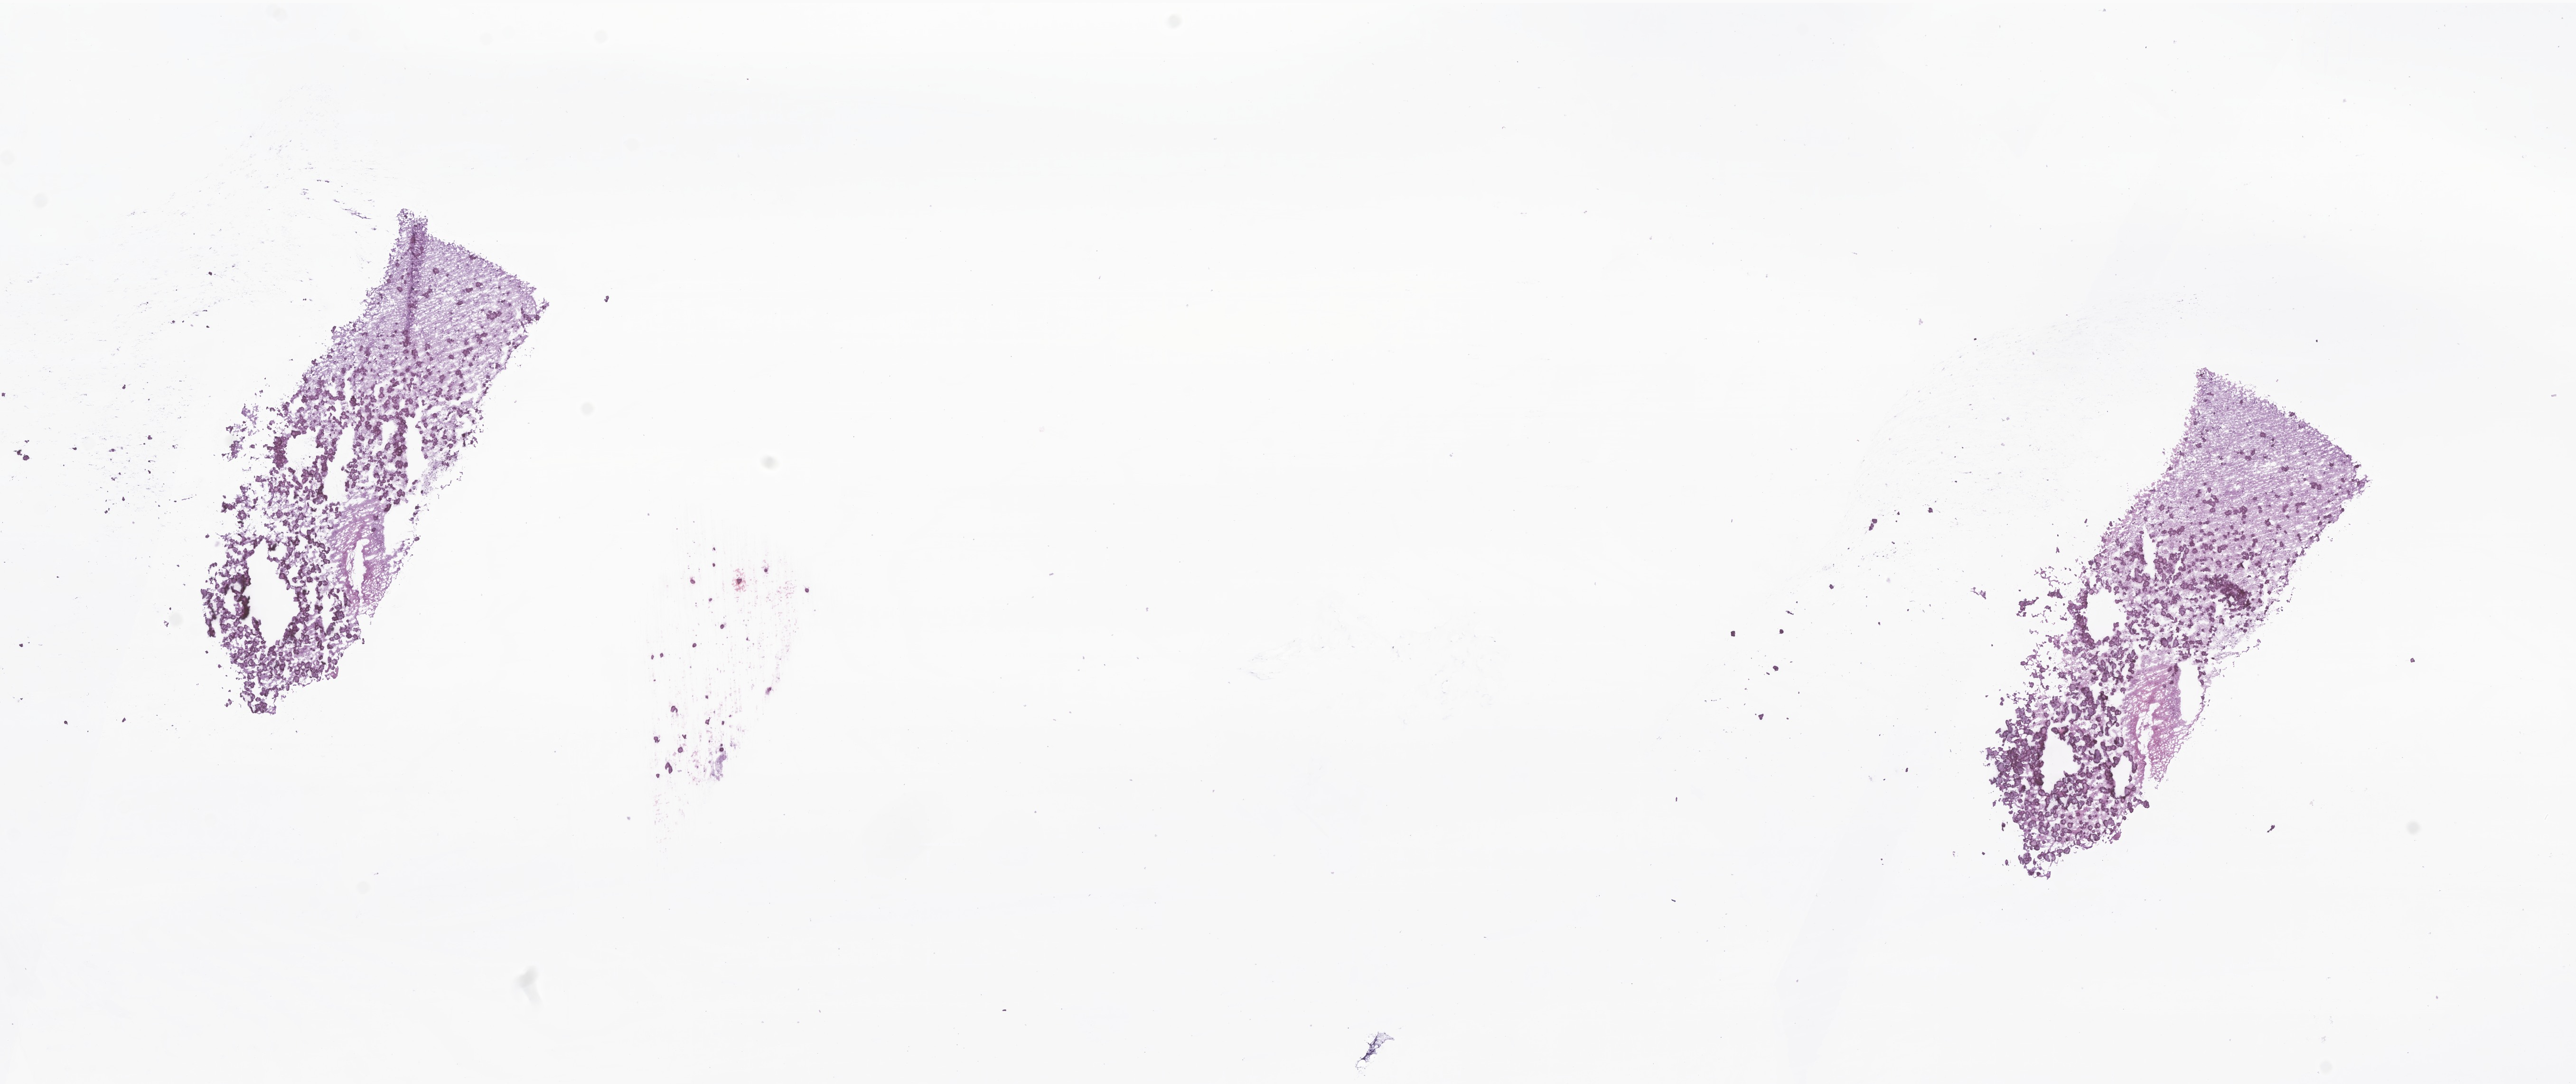
Whole-slide image, H&E stain of tumor tissue from the brain — whole scanned area (about 22.9 x 9.6 mm) shown as a low-resolution overview. Frozen section (OCT-embedded). Patient female; age 125 months (10 years 5 months).
• diagnosis: Neoplasm, uncertain whether benign or malignant